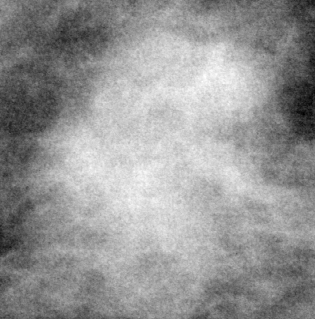
Crop from a digitized film mammogram around one marked abnormality; left breast; CC view.
- Marked abnormality: mass, shape lobulated, margins circumscribed / ill defined; BI-RADS assessment category 3; subtlety rating 3 on a 1 (subtle) to 5 (obvious) scale; pathology (as recorded): malignant.